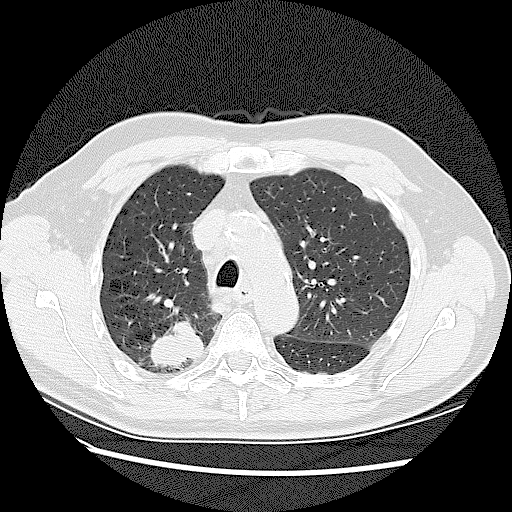
Low-dose screening chest CT, one axial slice; position 91 of 128 along the scan axis; reconstruction kernel LUNG; lung window (W 1500 / L -600 HU); 2.5 mm slice thickness; 512 × 512 image matrix, field of view 360 × 360 mm.
Structures marked on this image (expert manual segmentation):
- lesion 2 (tumor, upper lobe of right lung): box from (x=150, y=321) to (x=204, y=367) px